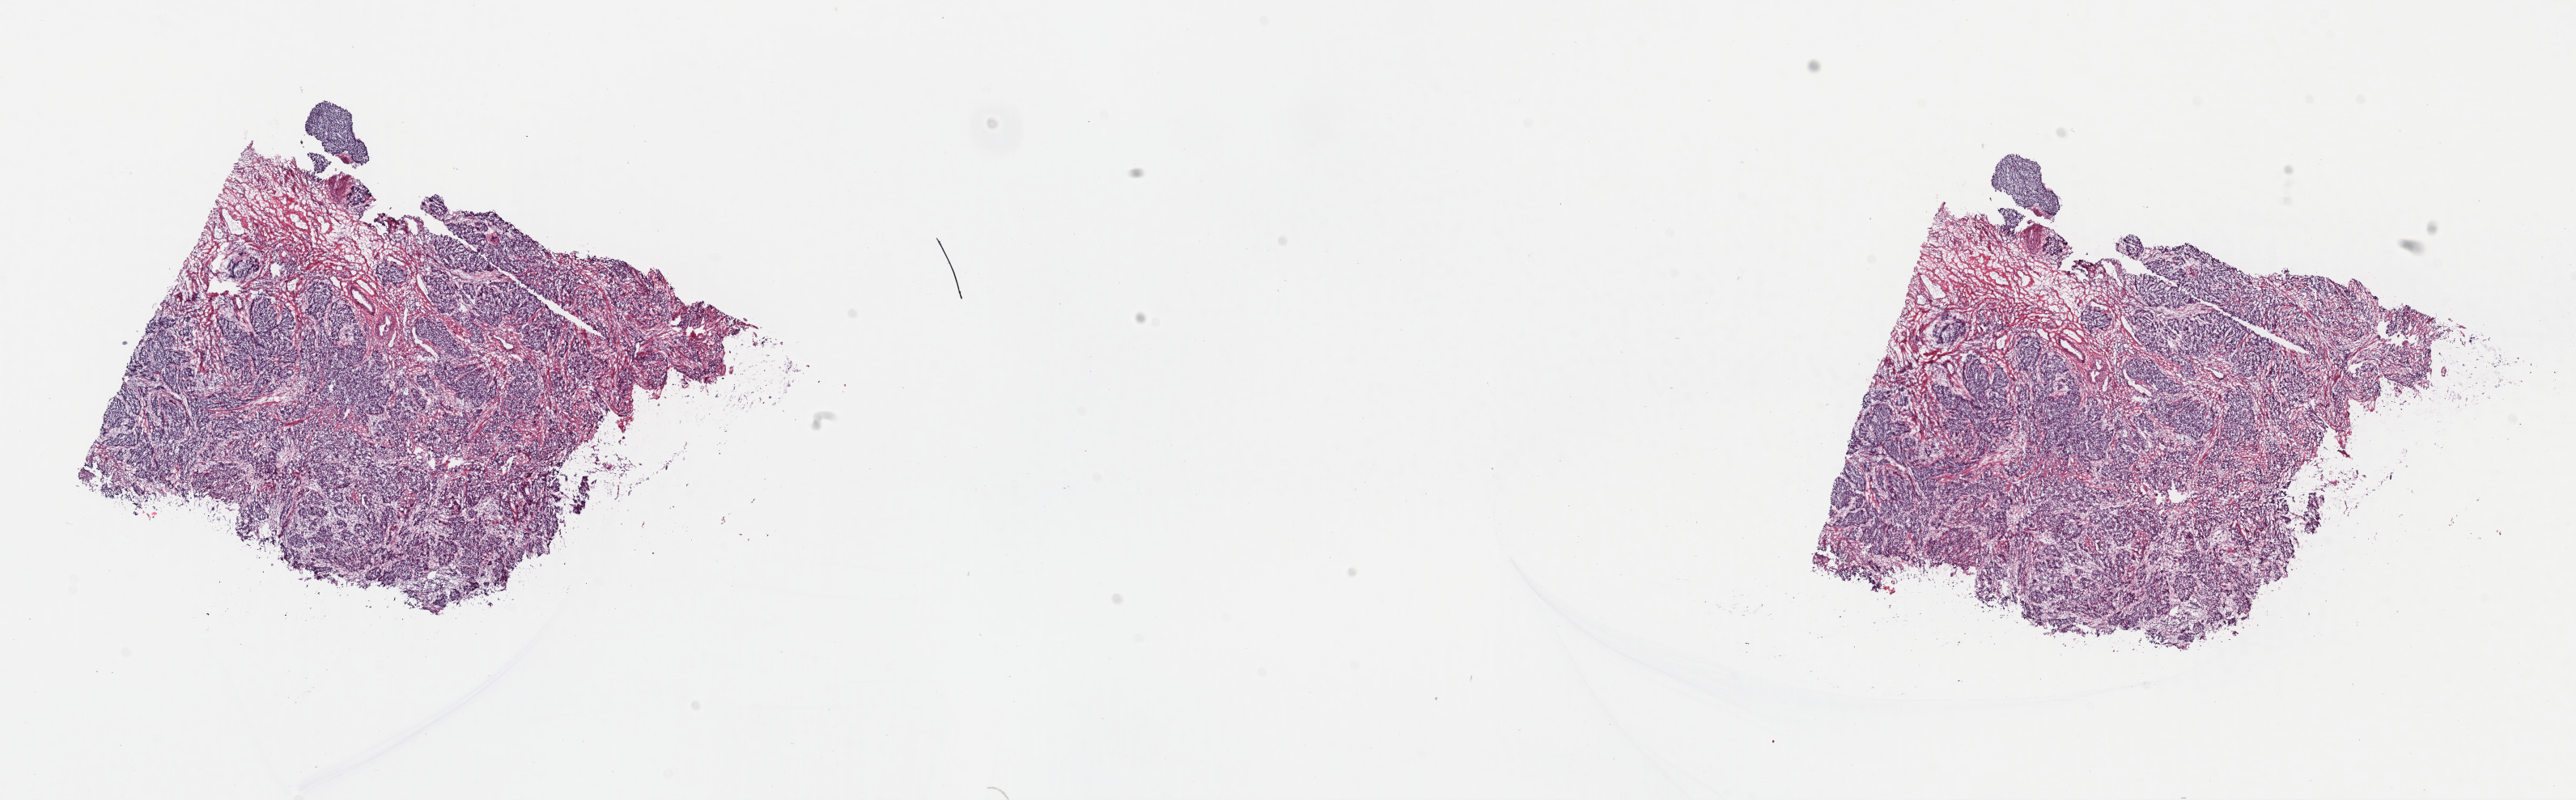
Digitized H&E-stained tissue section (whole slide) — shown as a low-resolution overview of the whole scanned area (about 25.0 x 7.8 mm, slide scanned at 40x), frozen section from the top of the tissue portion, cervix, primary tumour sample. Female, age 54 years at initial diagnosis. Slide review estimates, as recorded: tumour cells 60%, tumour nuclei 70%.
Diagnosis: Squamous cell carcinoma, NOS (cervix uteri).